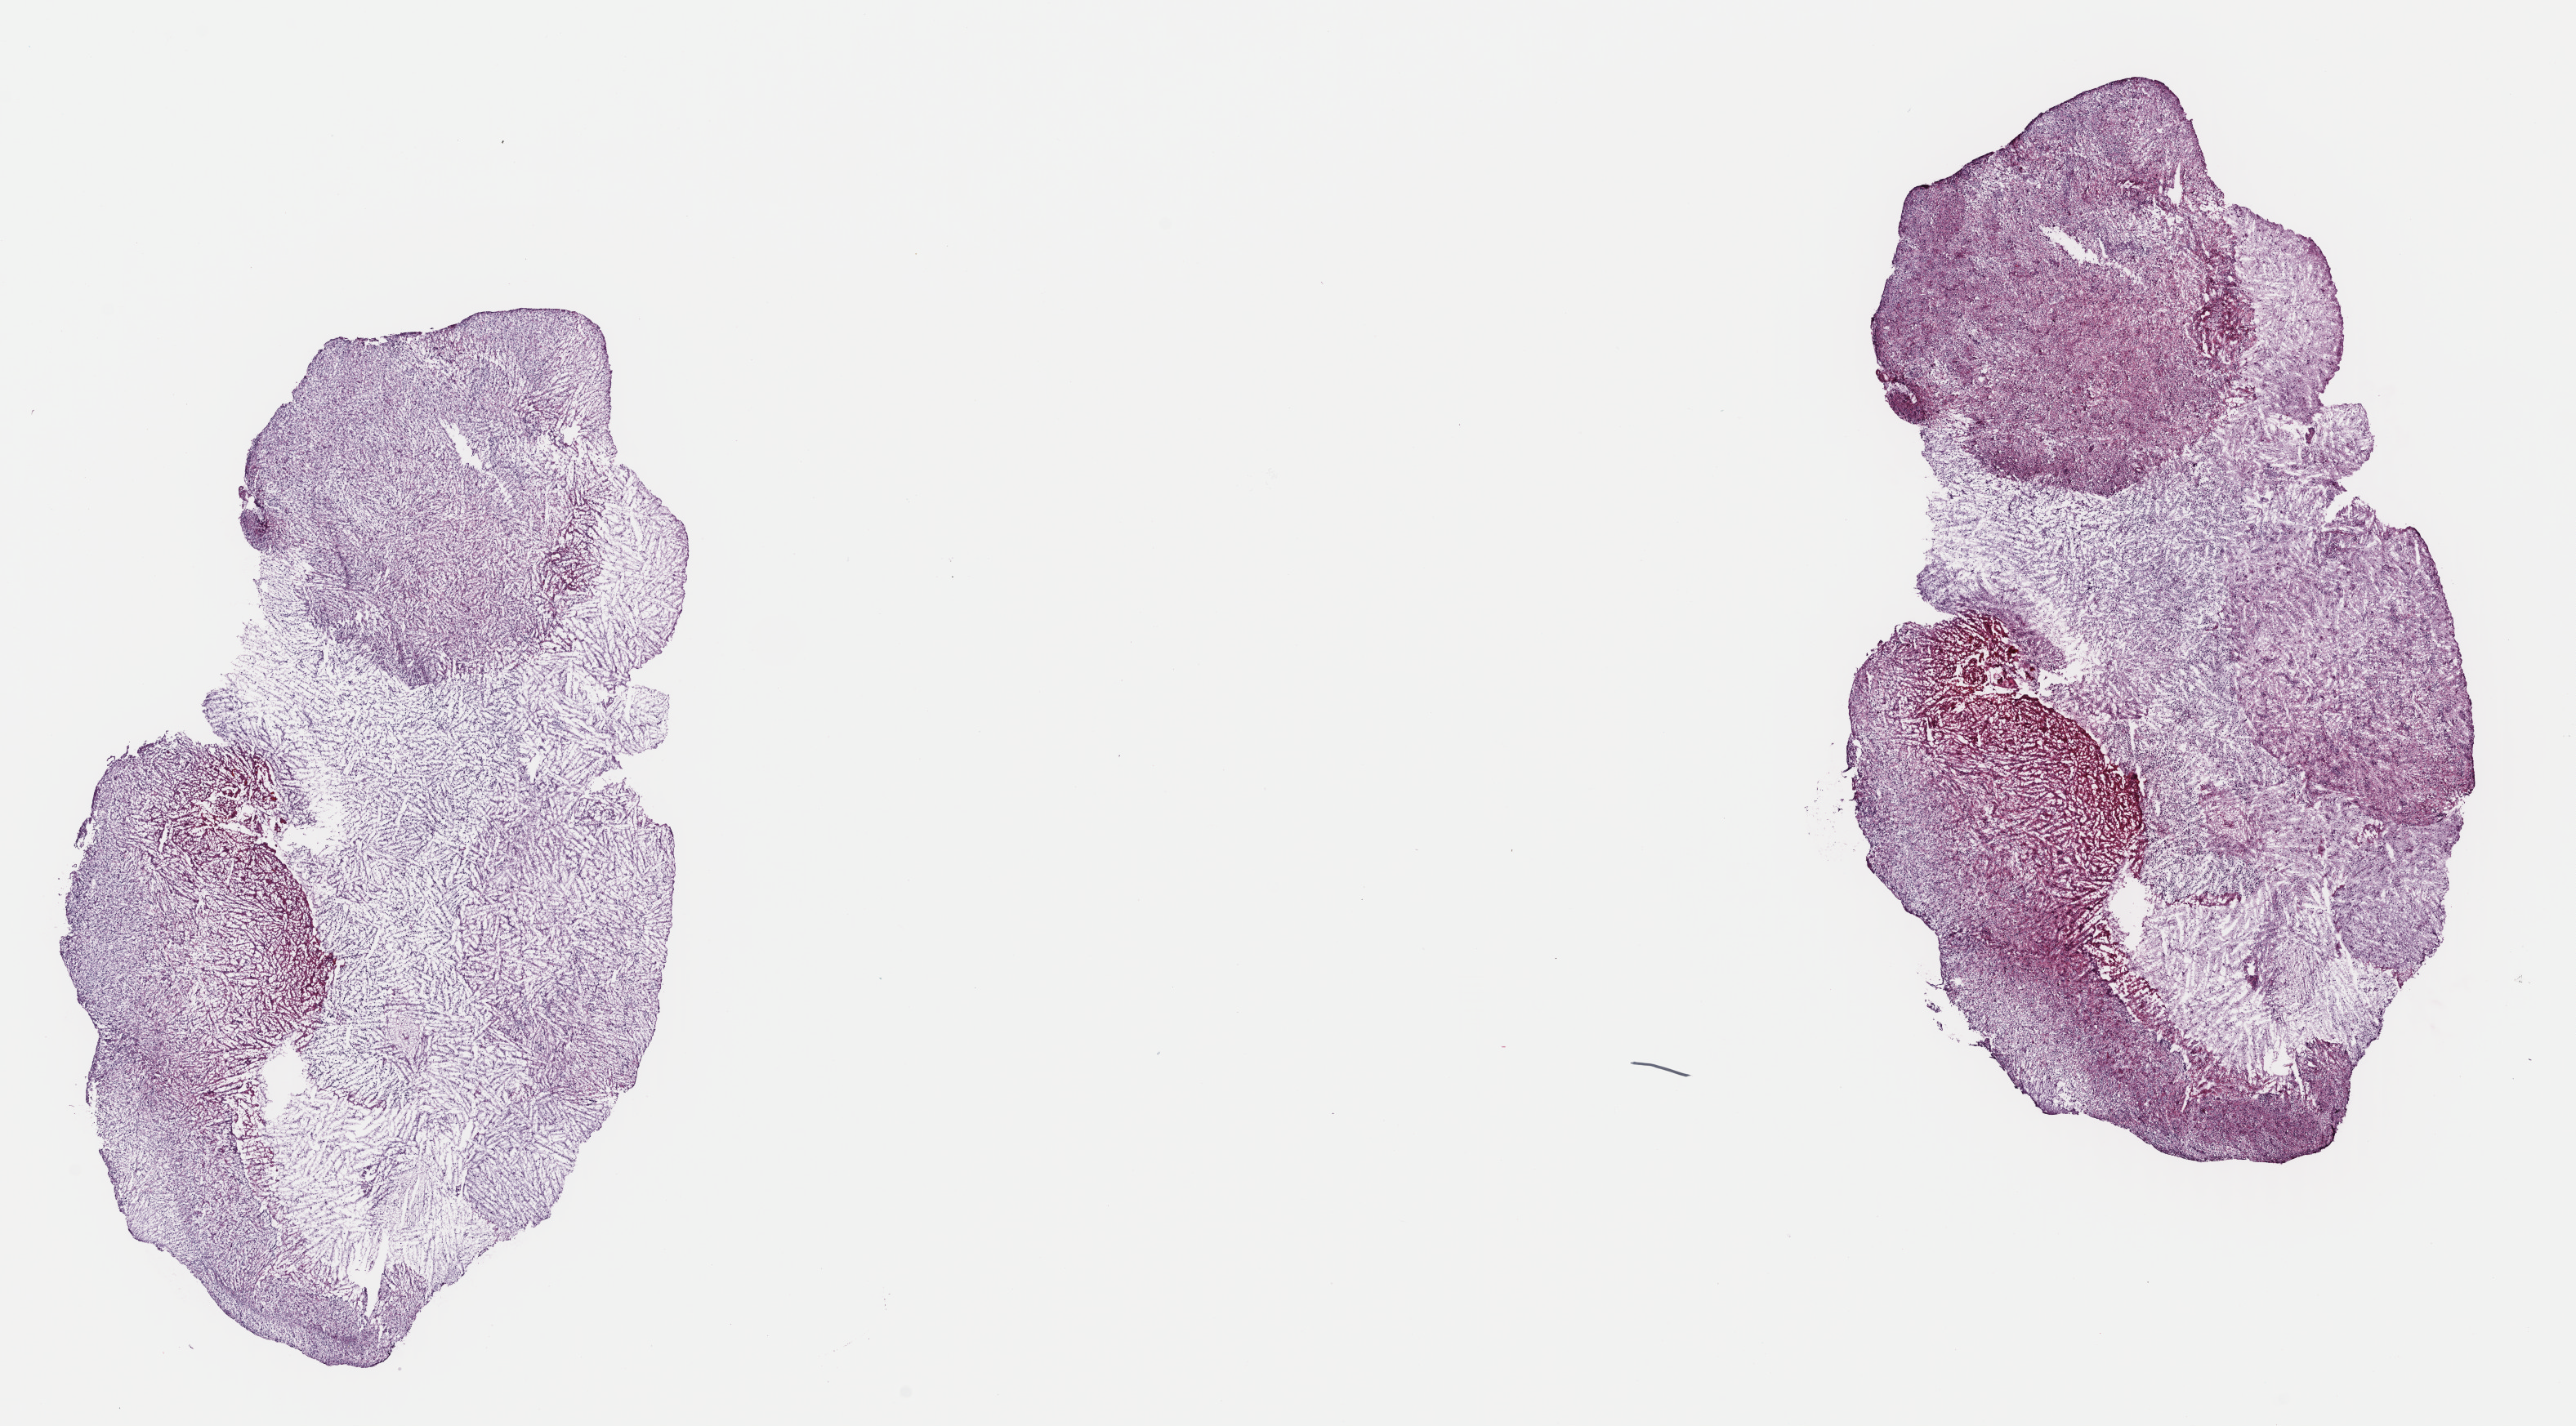
Hematoxylin and eosin (H&E) stained whole-slide image, low-resolution overview of the scanned area, about 24.9 x 13.8 mm (from a 40x scan). Frozen section. Primary tumour sample from the brain. Male, age 66 years at initial diagnosis.
Pathologic diagnosis: Astrocytoma, anaplastic (cerebrum).